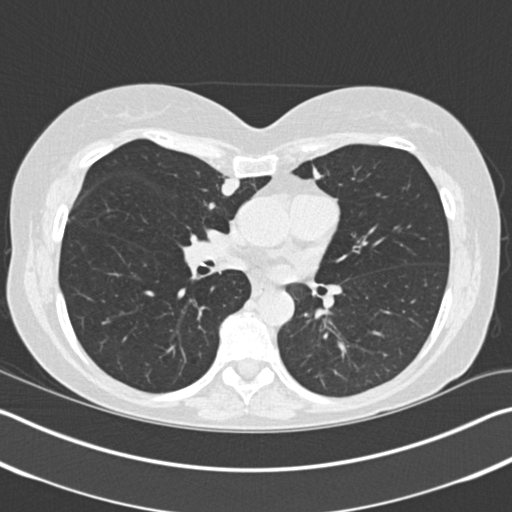
Low-dose screening chest CT, one axial slice. Slice 96 of 183 in the series (ordered by position). 120 kVp. Lung window (W 1500 / L -600 HU). 512 × 512 image matrix, field of view 340 × 340 mm.
Structures marked on this image (outlined manually by an expert reader):
- lesion 1 (tumor, upper lobe of right lung): bounding box [x1, y1, x2, y2] px = [222, 177, 240, 196]